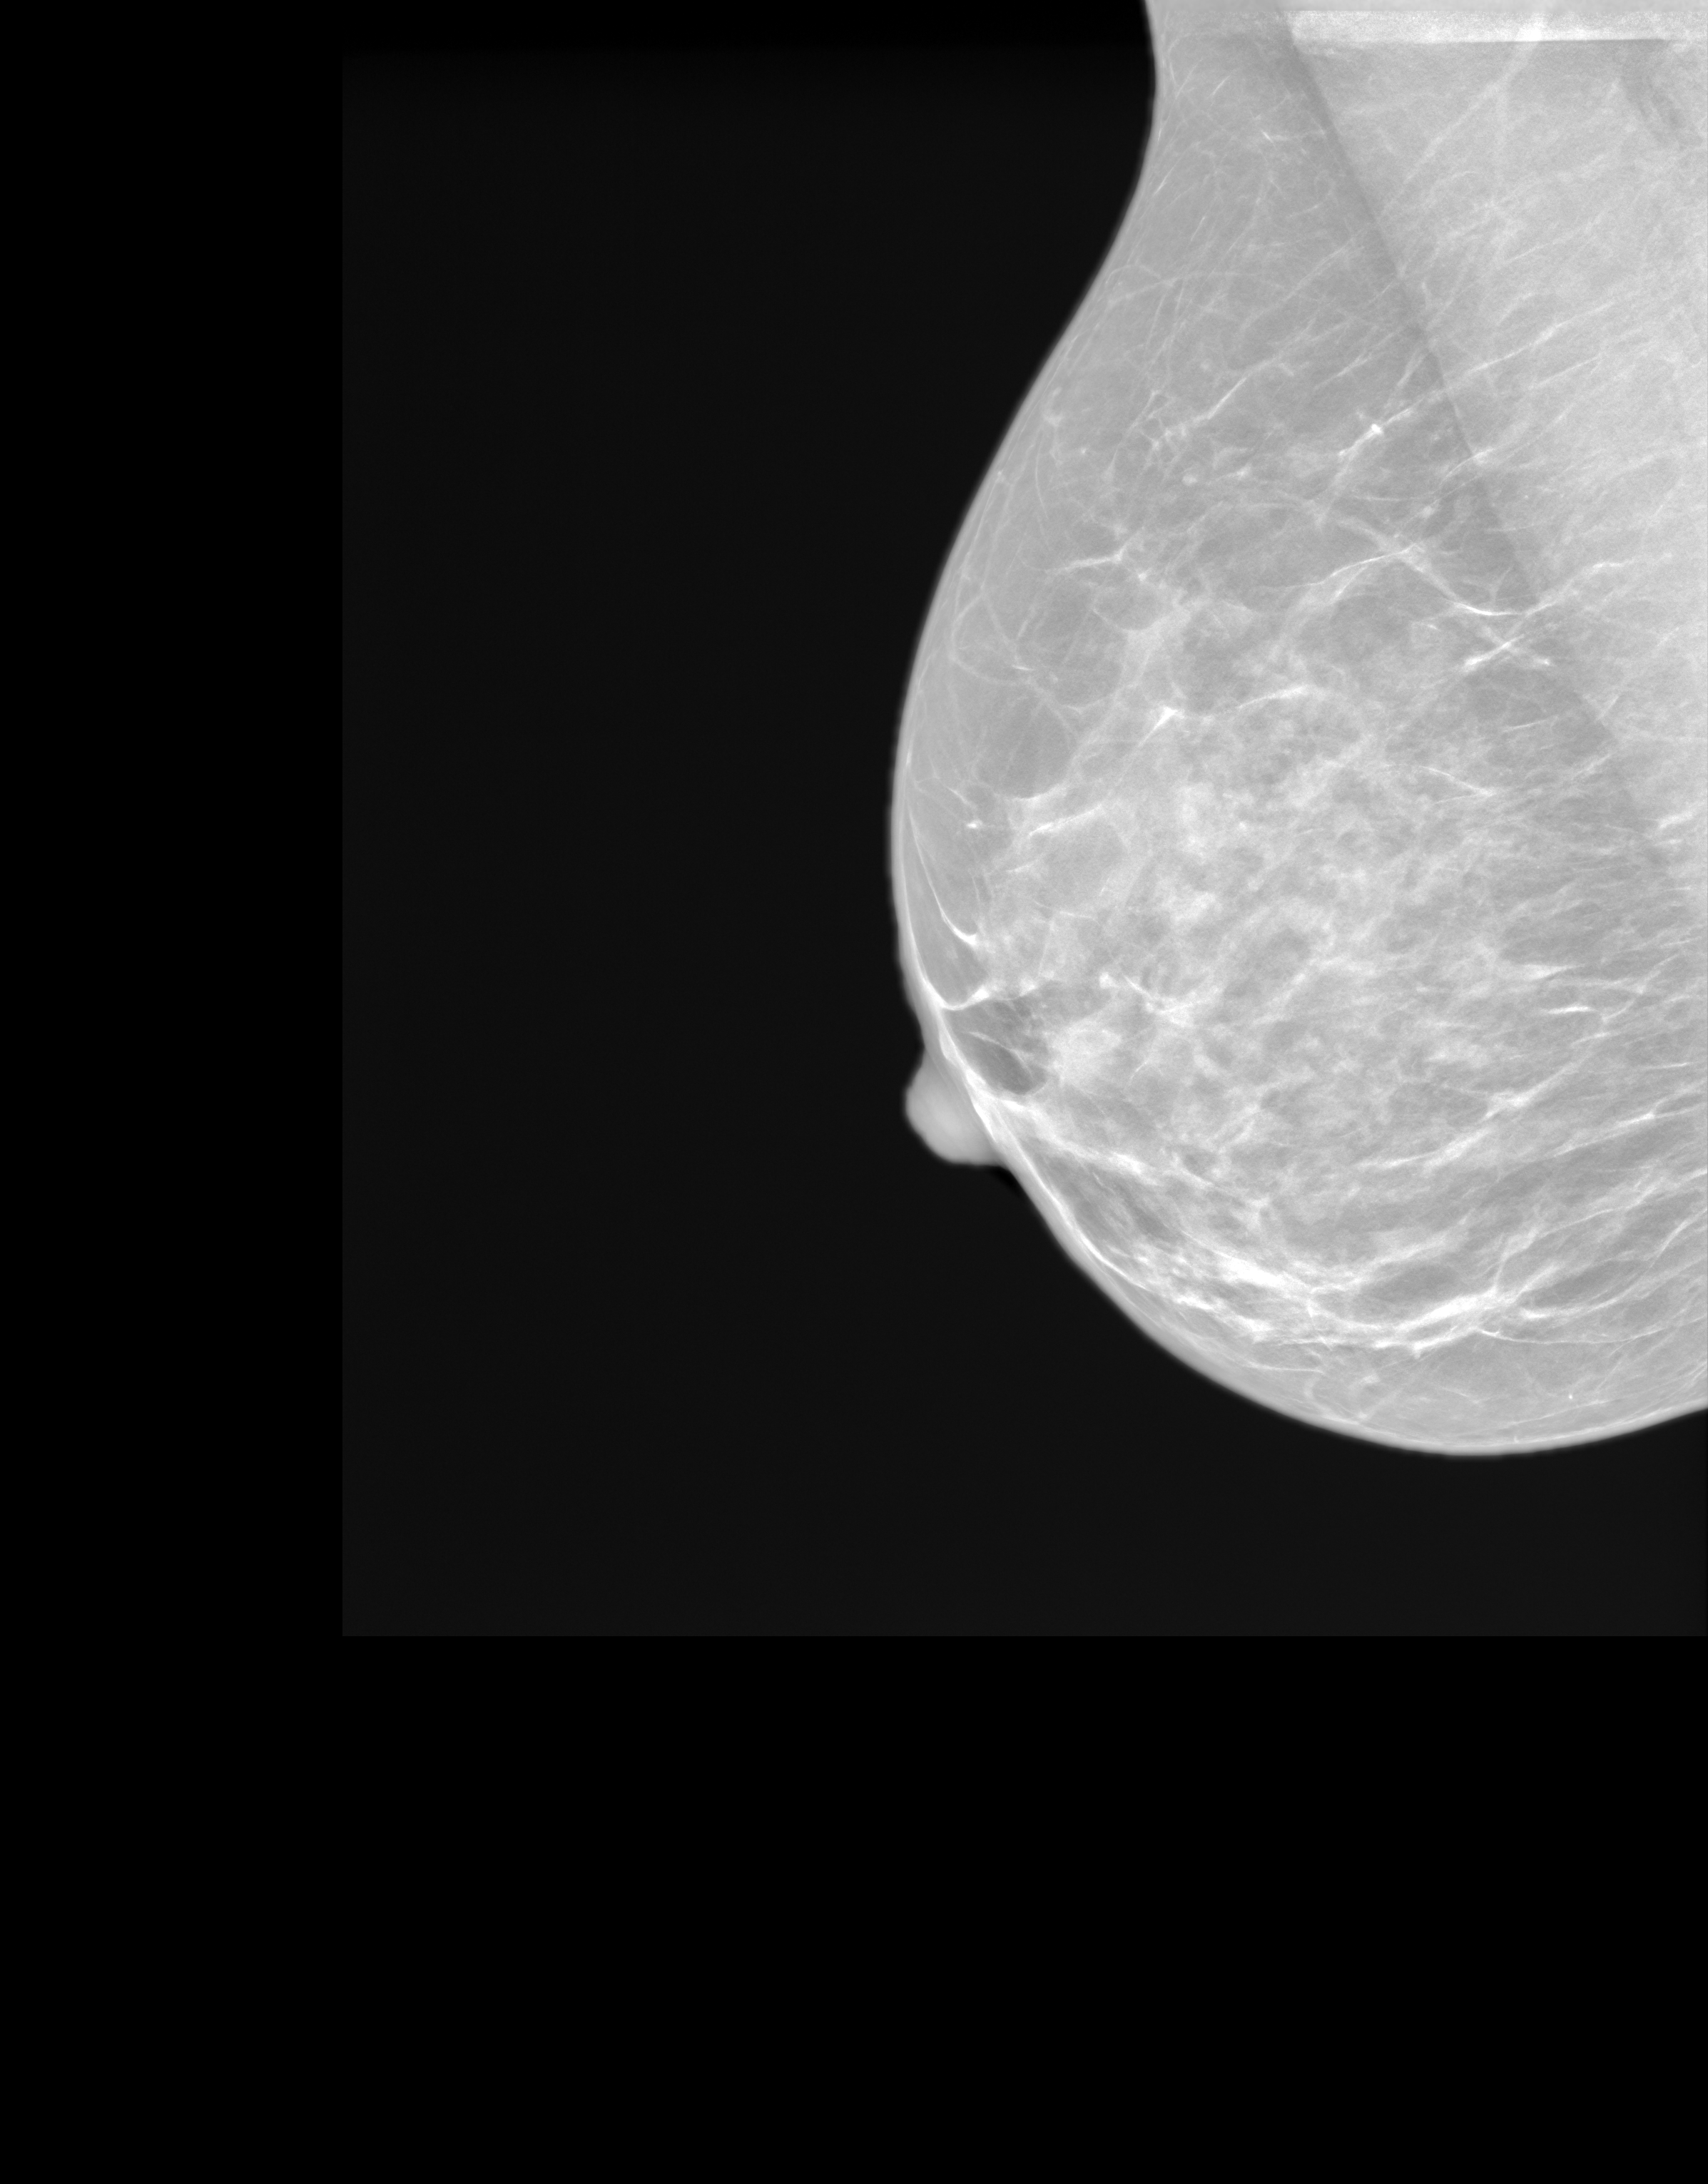
Synthesized 2-D mammogram reconstructed from digital breast tomosynthesis; right breast; MLO view; screening examination; system: SenoIris_1SP1.1(421). Patient: female, 53 years.
Breast density at the screening exam (both breasts): heterogeneously dense (BI-RADS density category c). Final BI-RADS assessment for this screening round (tomosynthesis exam, both breasts): category 1. Recall: no recall after this screen.